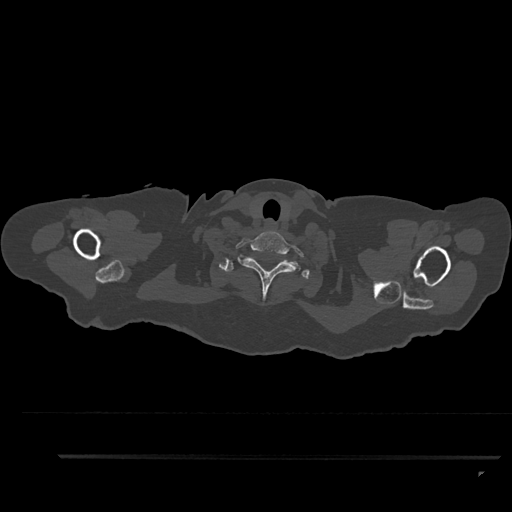
CT including the spine, one axial slice; slice 786 of 797 in the series (ordered by position); reconstruction kernel Br40s/3; 120 kVp; bone window (W 1800 / L 400 HU); 0.5 mm slice thickness; 512 × 512 image matrix, field of view 408 × 408 mm. Female patient, age 44 years. From the clinical record (not read from this slice): primary cancer: renal.
Outlined on this slice (semi-automatically segmented with operator editing):
- T1 vertebra: box from (x=219, y=255) to (x=309, y=279) px